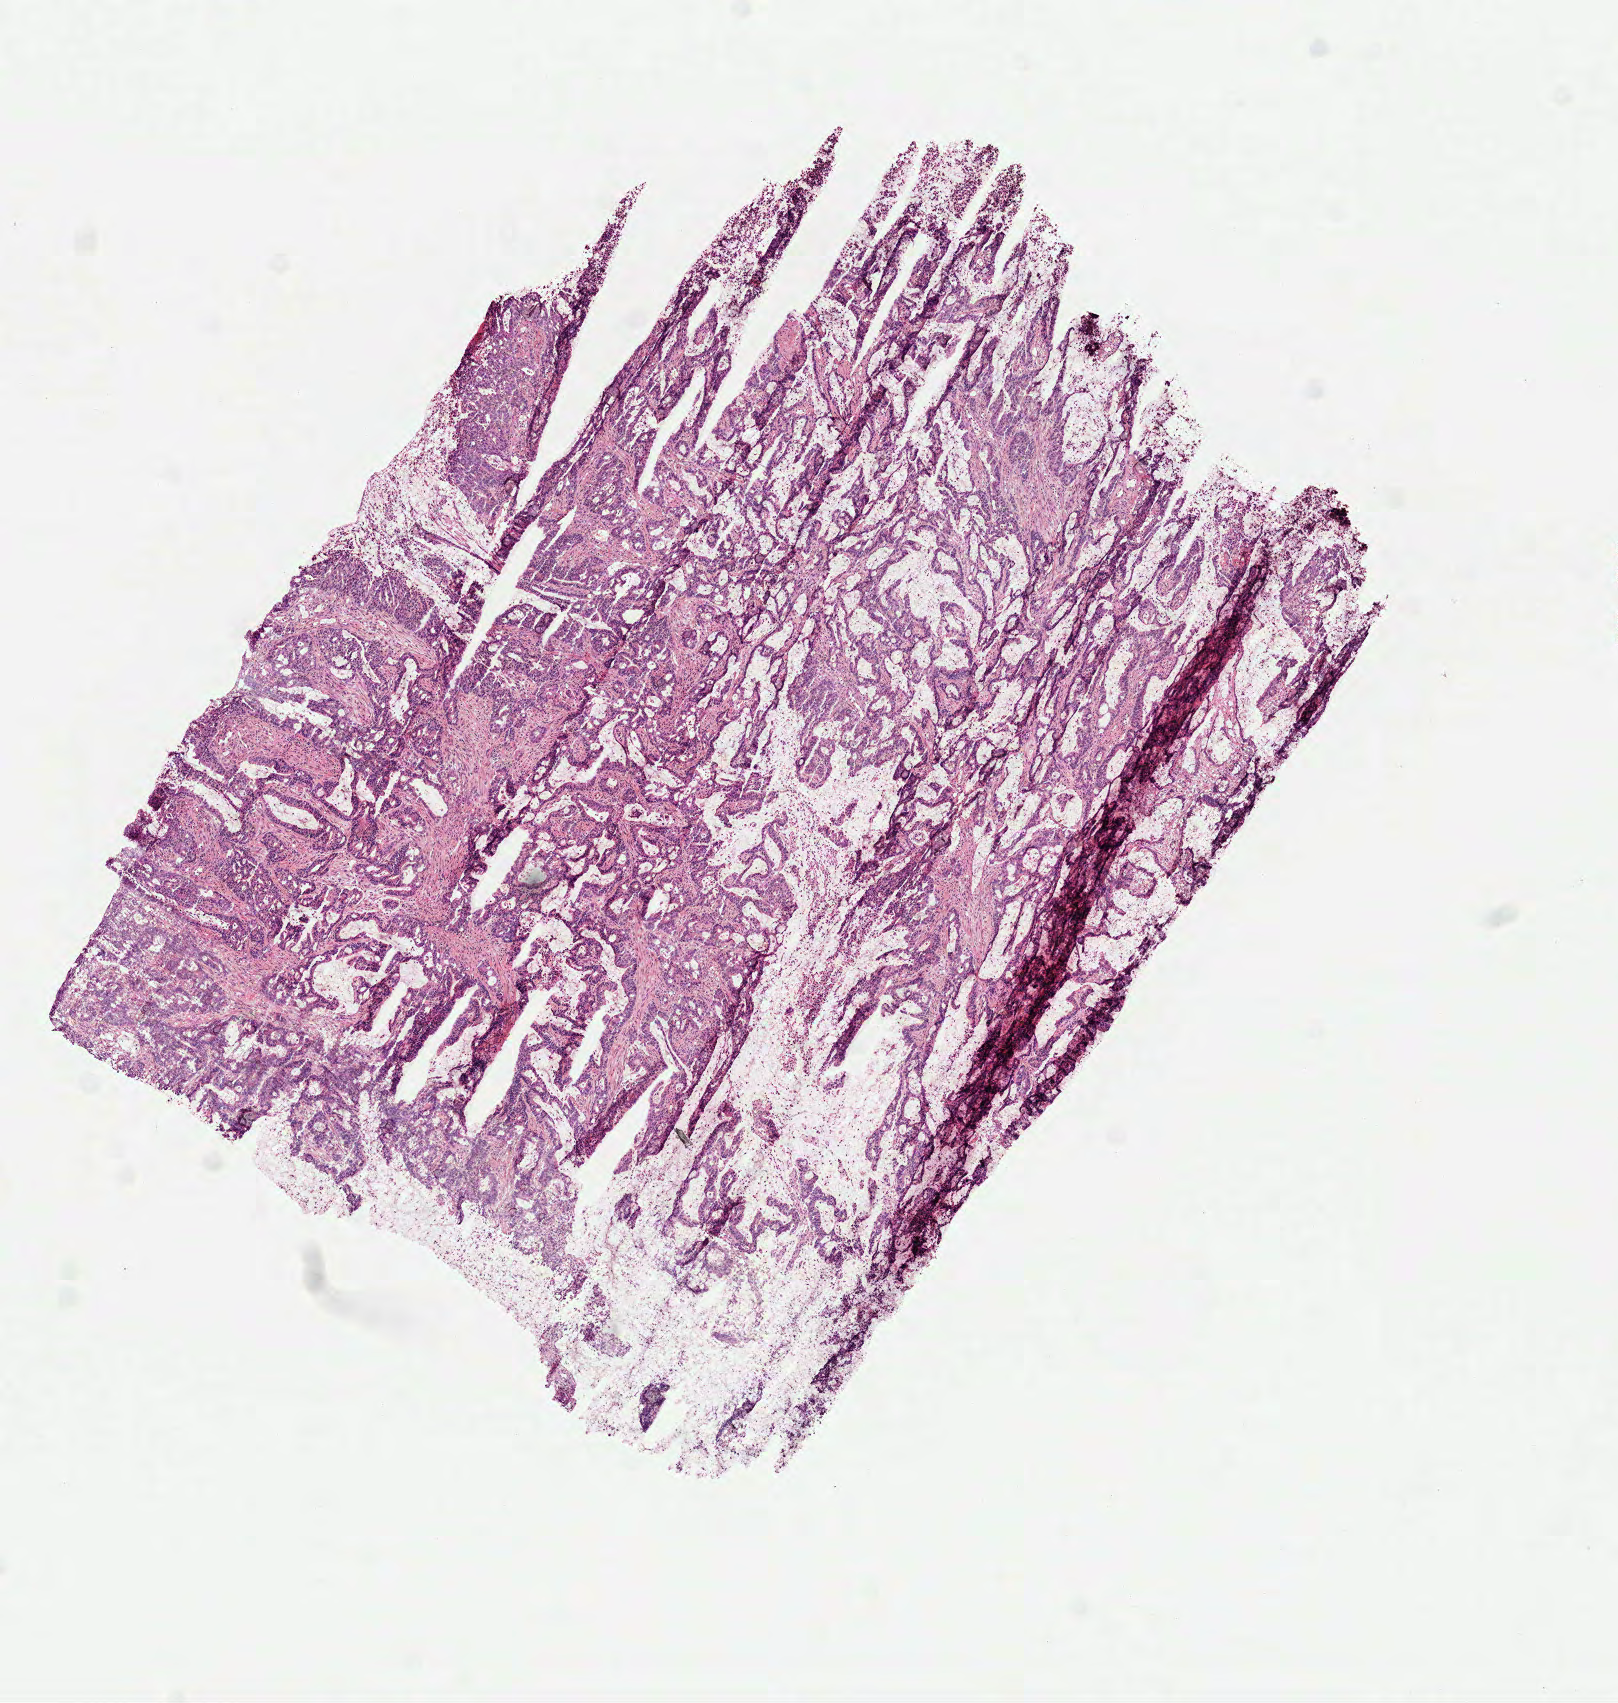
Digitized H&E tissue section (whole slide), whole scanned area (about 6.5 x 6.9 mm) shown as a low-resolution overview, frozen section from the top of the tissue portion, primary tumour sample from the colon. Male, age 66 years at initial diagnosis. Pathologist review of this section (percent, as recorded): tumour cells 99%, tumour nuclei 80%, normal cells 0%, stromal cells 0%, necrosis 1%. Infiltration values recorded for this section: lymphocyte infiltration 10%, monocyte infiltration 2%, neutrophil infiltration 5%.
- histologic diagnosis: Mucinous adenocarcinoma (cecum)
- lymph nodes positive (case pathology): 0 of 13 examined
- AJCC pathologic stage: I